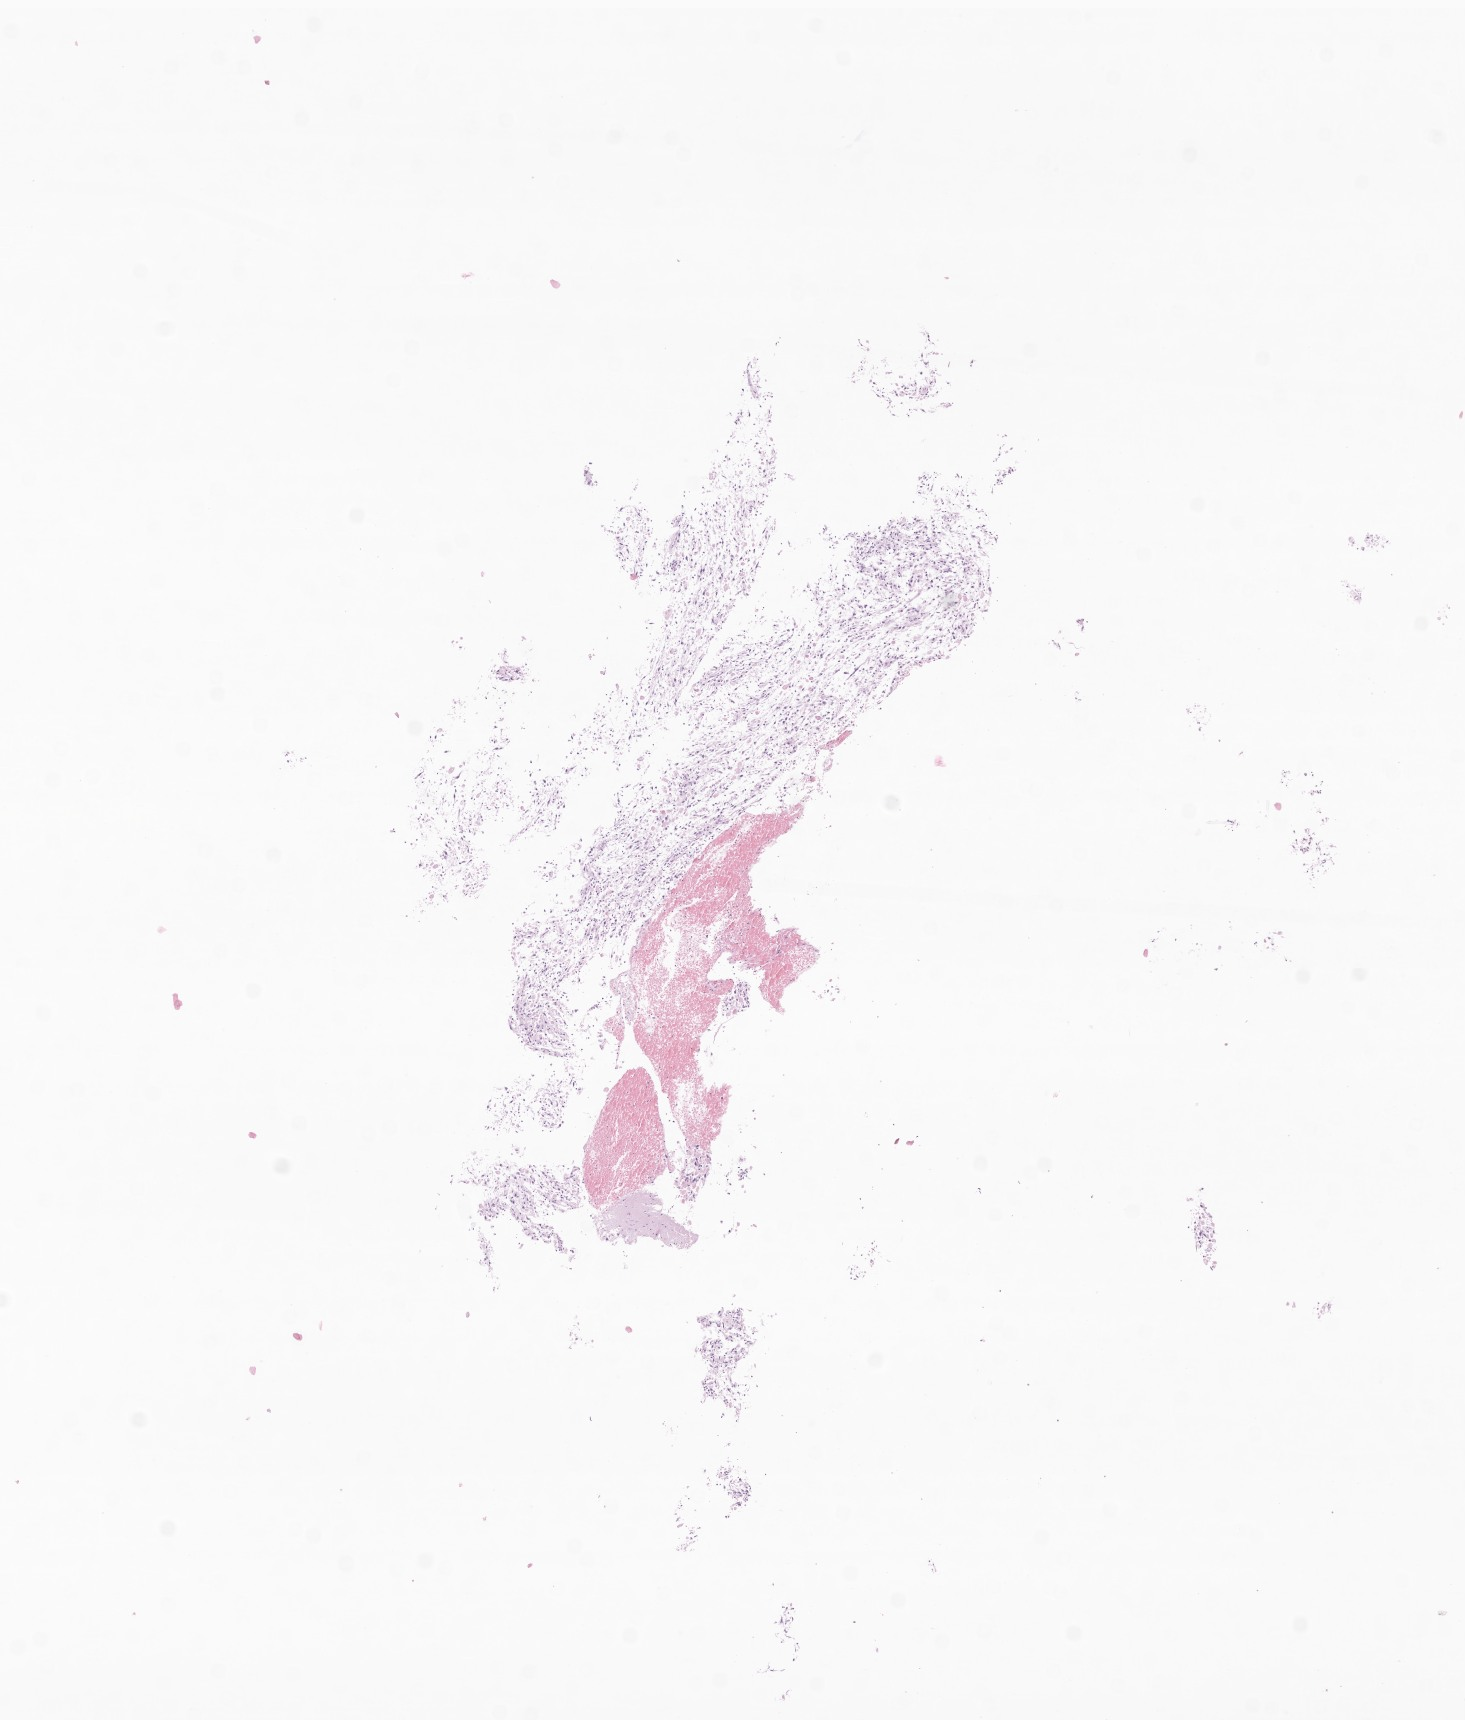
Digitized haematoxylin and eosin-stained section of tumor tissue from the temporal lobe — a low-resolution overview of the entire scanned area, about 6.2 x 7.3 mm, formalin-fixed paraffin-embedded section. Patient male; age 185 months (15 years 5 months).
Recorded diagnosis: Ganglioglioma, NOS.